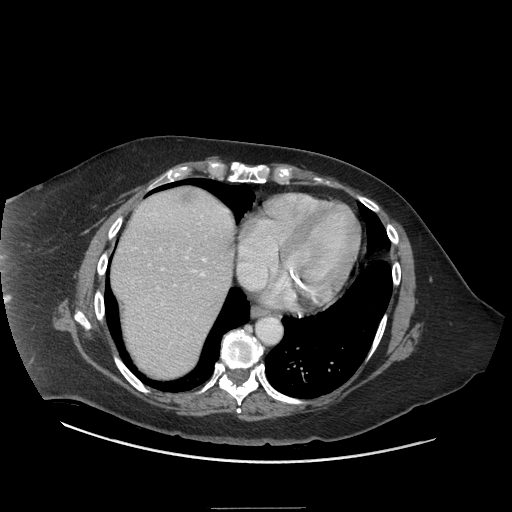
Contrast-enhanced abdominal CT (liver protocol), one axial slice; position 64 of 81 along the scan axis; 140 kVp; soft-tissue window (W 400 / L 40 HU); 512 × 512 image matrix. From the clinical record (not read from this slice): diagnosis: hepatocellular carcinoma (patient treated with transarterial chemoembolisation; whether this scan precedes or follows treatment is not stated here); TNM stage (as recorded): Stage-II; Child-Pugh class: A; tumour nodularity: multinodular.
Outlined on this slice (semi-automatically segmented with operator editing):
- abdominal aorta: bounding box [x1, y1, x2, y2] px = [257, 318, 281, 344]
- liver parenchyma outside the tumour (the mass and vessels are separate outlines, so this box may not span the whole liver): [110, 188, 234, 378]
- mass: [174, 187, 199, 204]
- liver vessels: [131, 206, 231, 335]